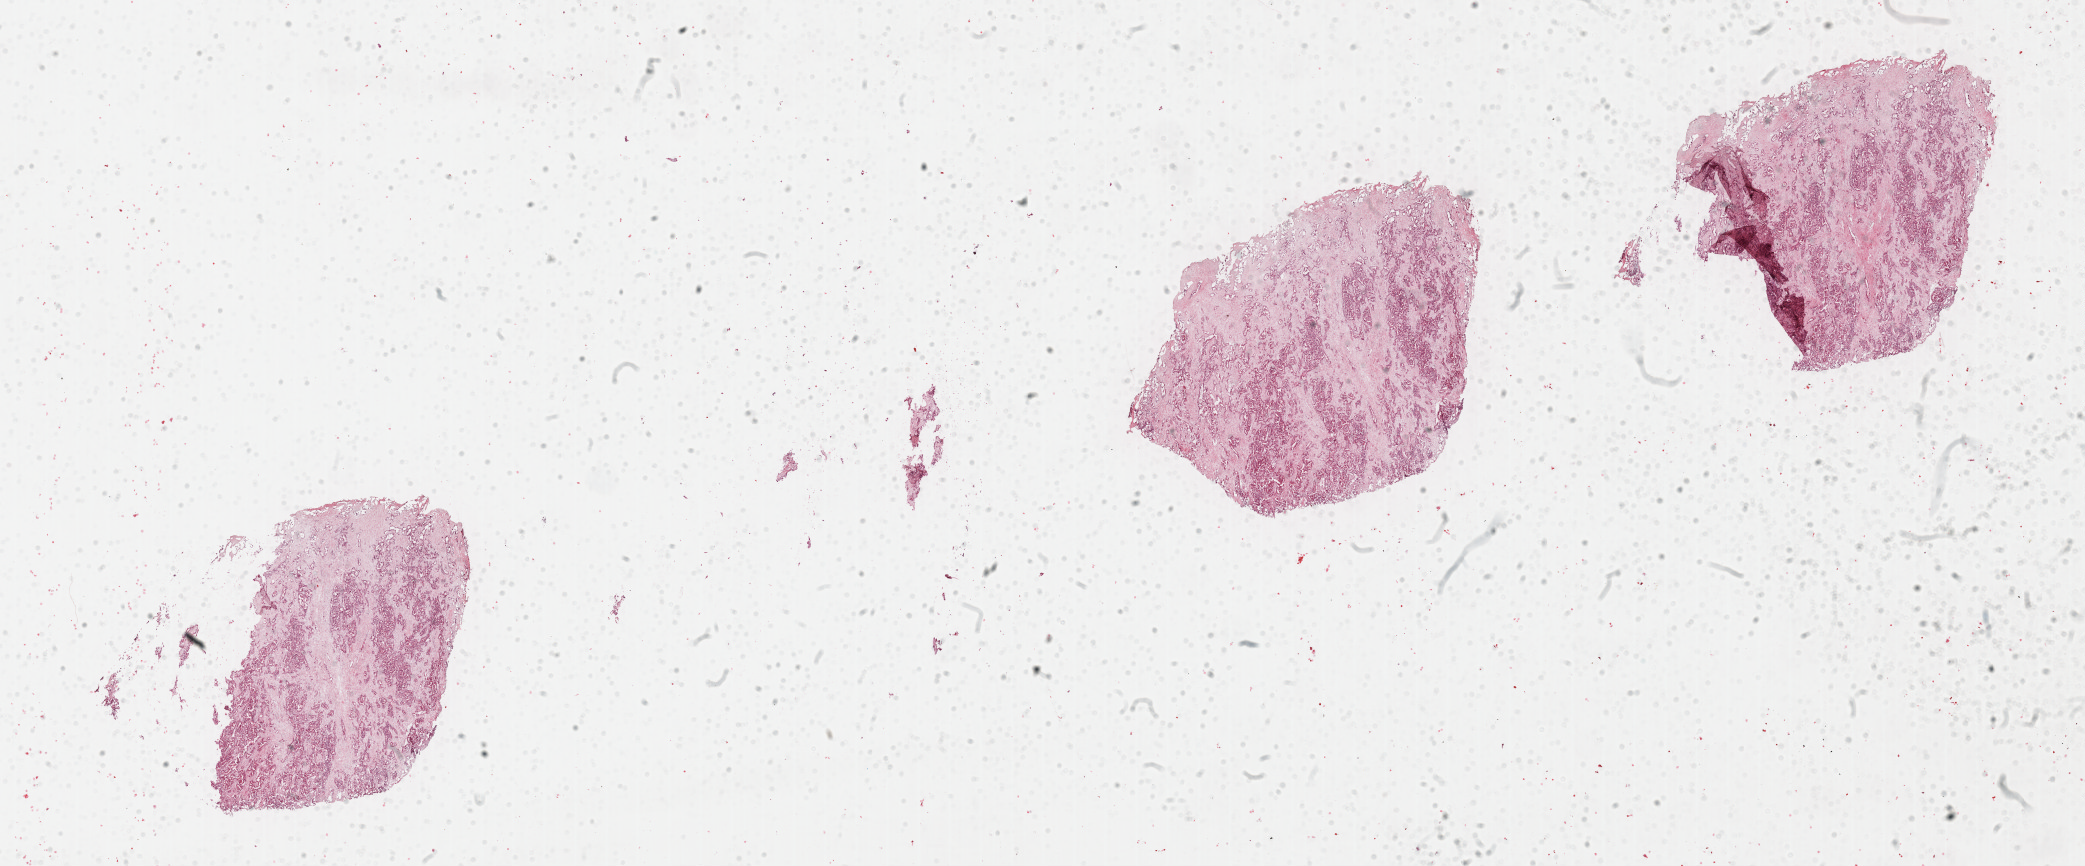
Whole-slide histology image, H&E-stained, a low-resolution overview of the entire scanned area, about 33.7 x 14.0 mm. FFPE section. Bile duct, primary tumour sample. Patient: female, age at initial diagnosis 71 years. Histologic grade: G2 (moderately differentiated).
• TNM: T2a N0 M0
• AJCC pathologic stage: II (7th edition)
• histologic diagnosis: Cholangiocarcinoma (intrahepatic bile duct)